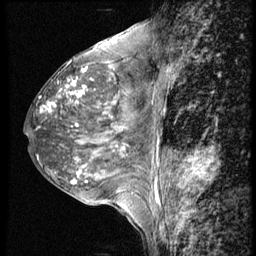
Breast MRI (dynamic contrast-enhanced), one sagittal slice. Slice 23 of 56 in the series (ordered by position). 4 images stored at this slice position (order not interpretable as contrast timing). 1.5 T. TE 4.2 ms, TR 9 ms. 2.5 mm slice thickness. 256 × 256 image matrix. Patient: female, 50 years. From the clinical record (not read from this slice): setting: breast cancer imaged before/during neoadjuvant chemotherapy; receptor status: triple-negative.
Outlined on this slice (semi-automatic segmentation, software-assisted and operator-edited):
- analysis volume of interest (the breast-tissue region the enhancement analysis was run in; not a lesion): bounding box [x1, y1, x2, y2] px = [23, 46, 148, 188]
- tumour enhancement mask (voxels above the 140 % enhancement threshold inside the analysis volume of interest): [41, 83, 125, 184]